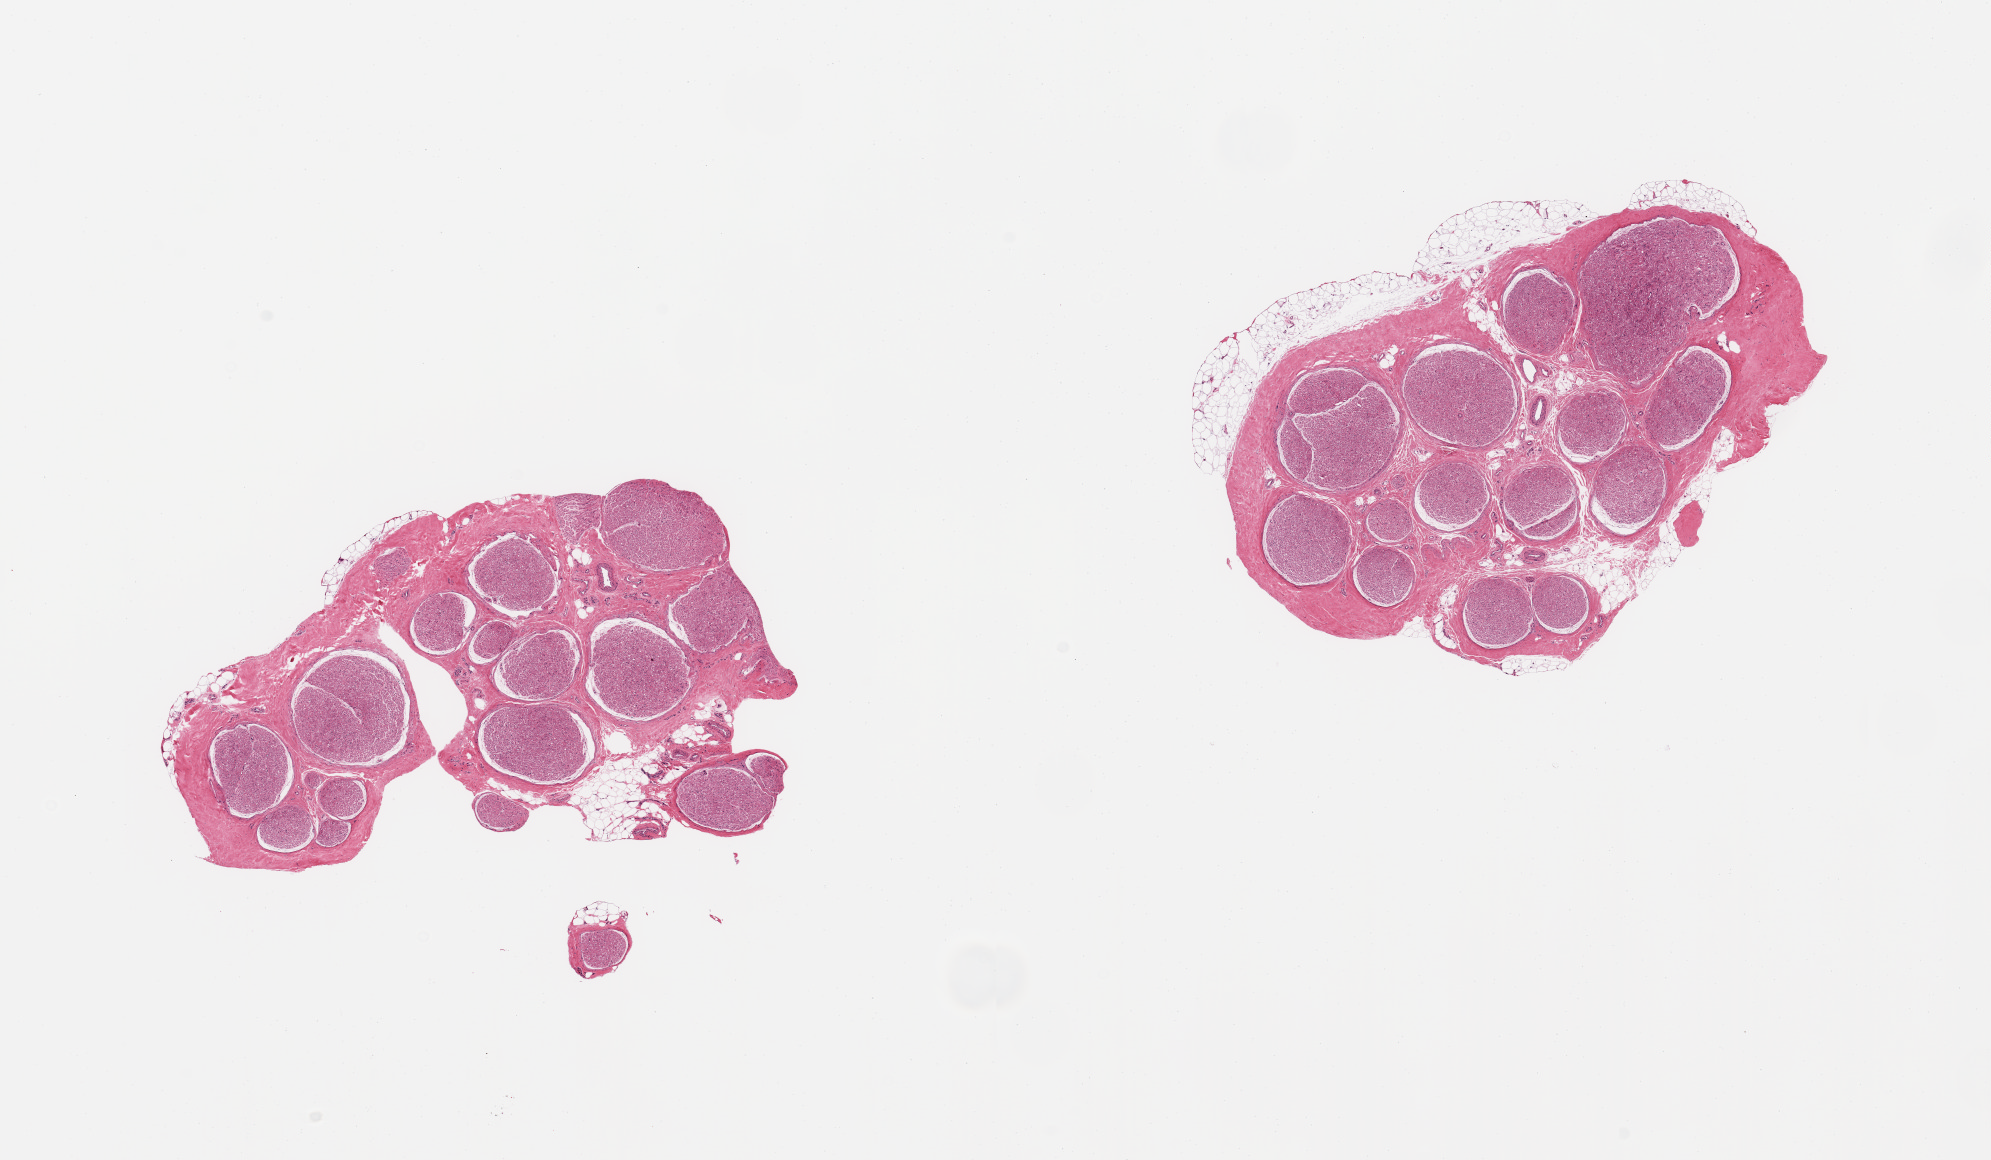
H&E whole-slide image, brightfield, a low-resolution overview of the entire scanned area, about 15.8 x 9.2 mm. PAXgene-fixed, paraffin-embedded tissue. Section of tibial nerve (target tissue). Tissue donor sample.
Pathologist's review note for this sample: 2 pieces; ~20% and 30% prineurium and external fat.